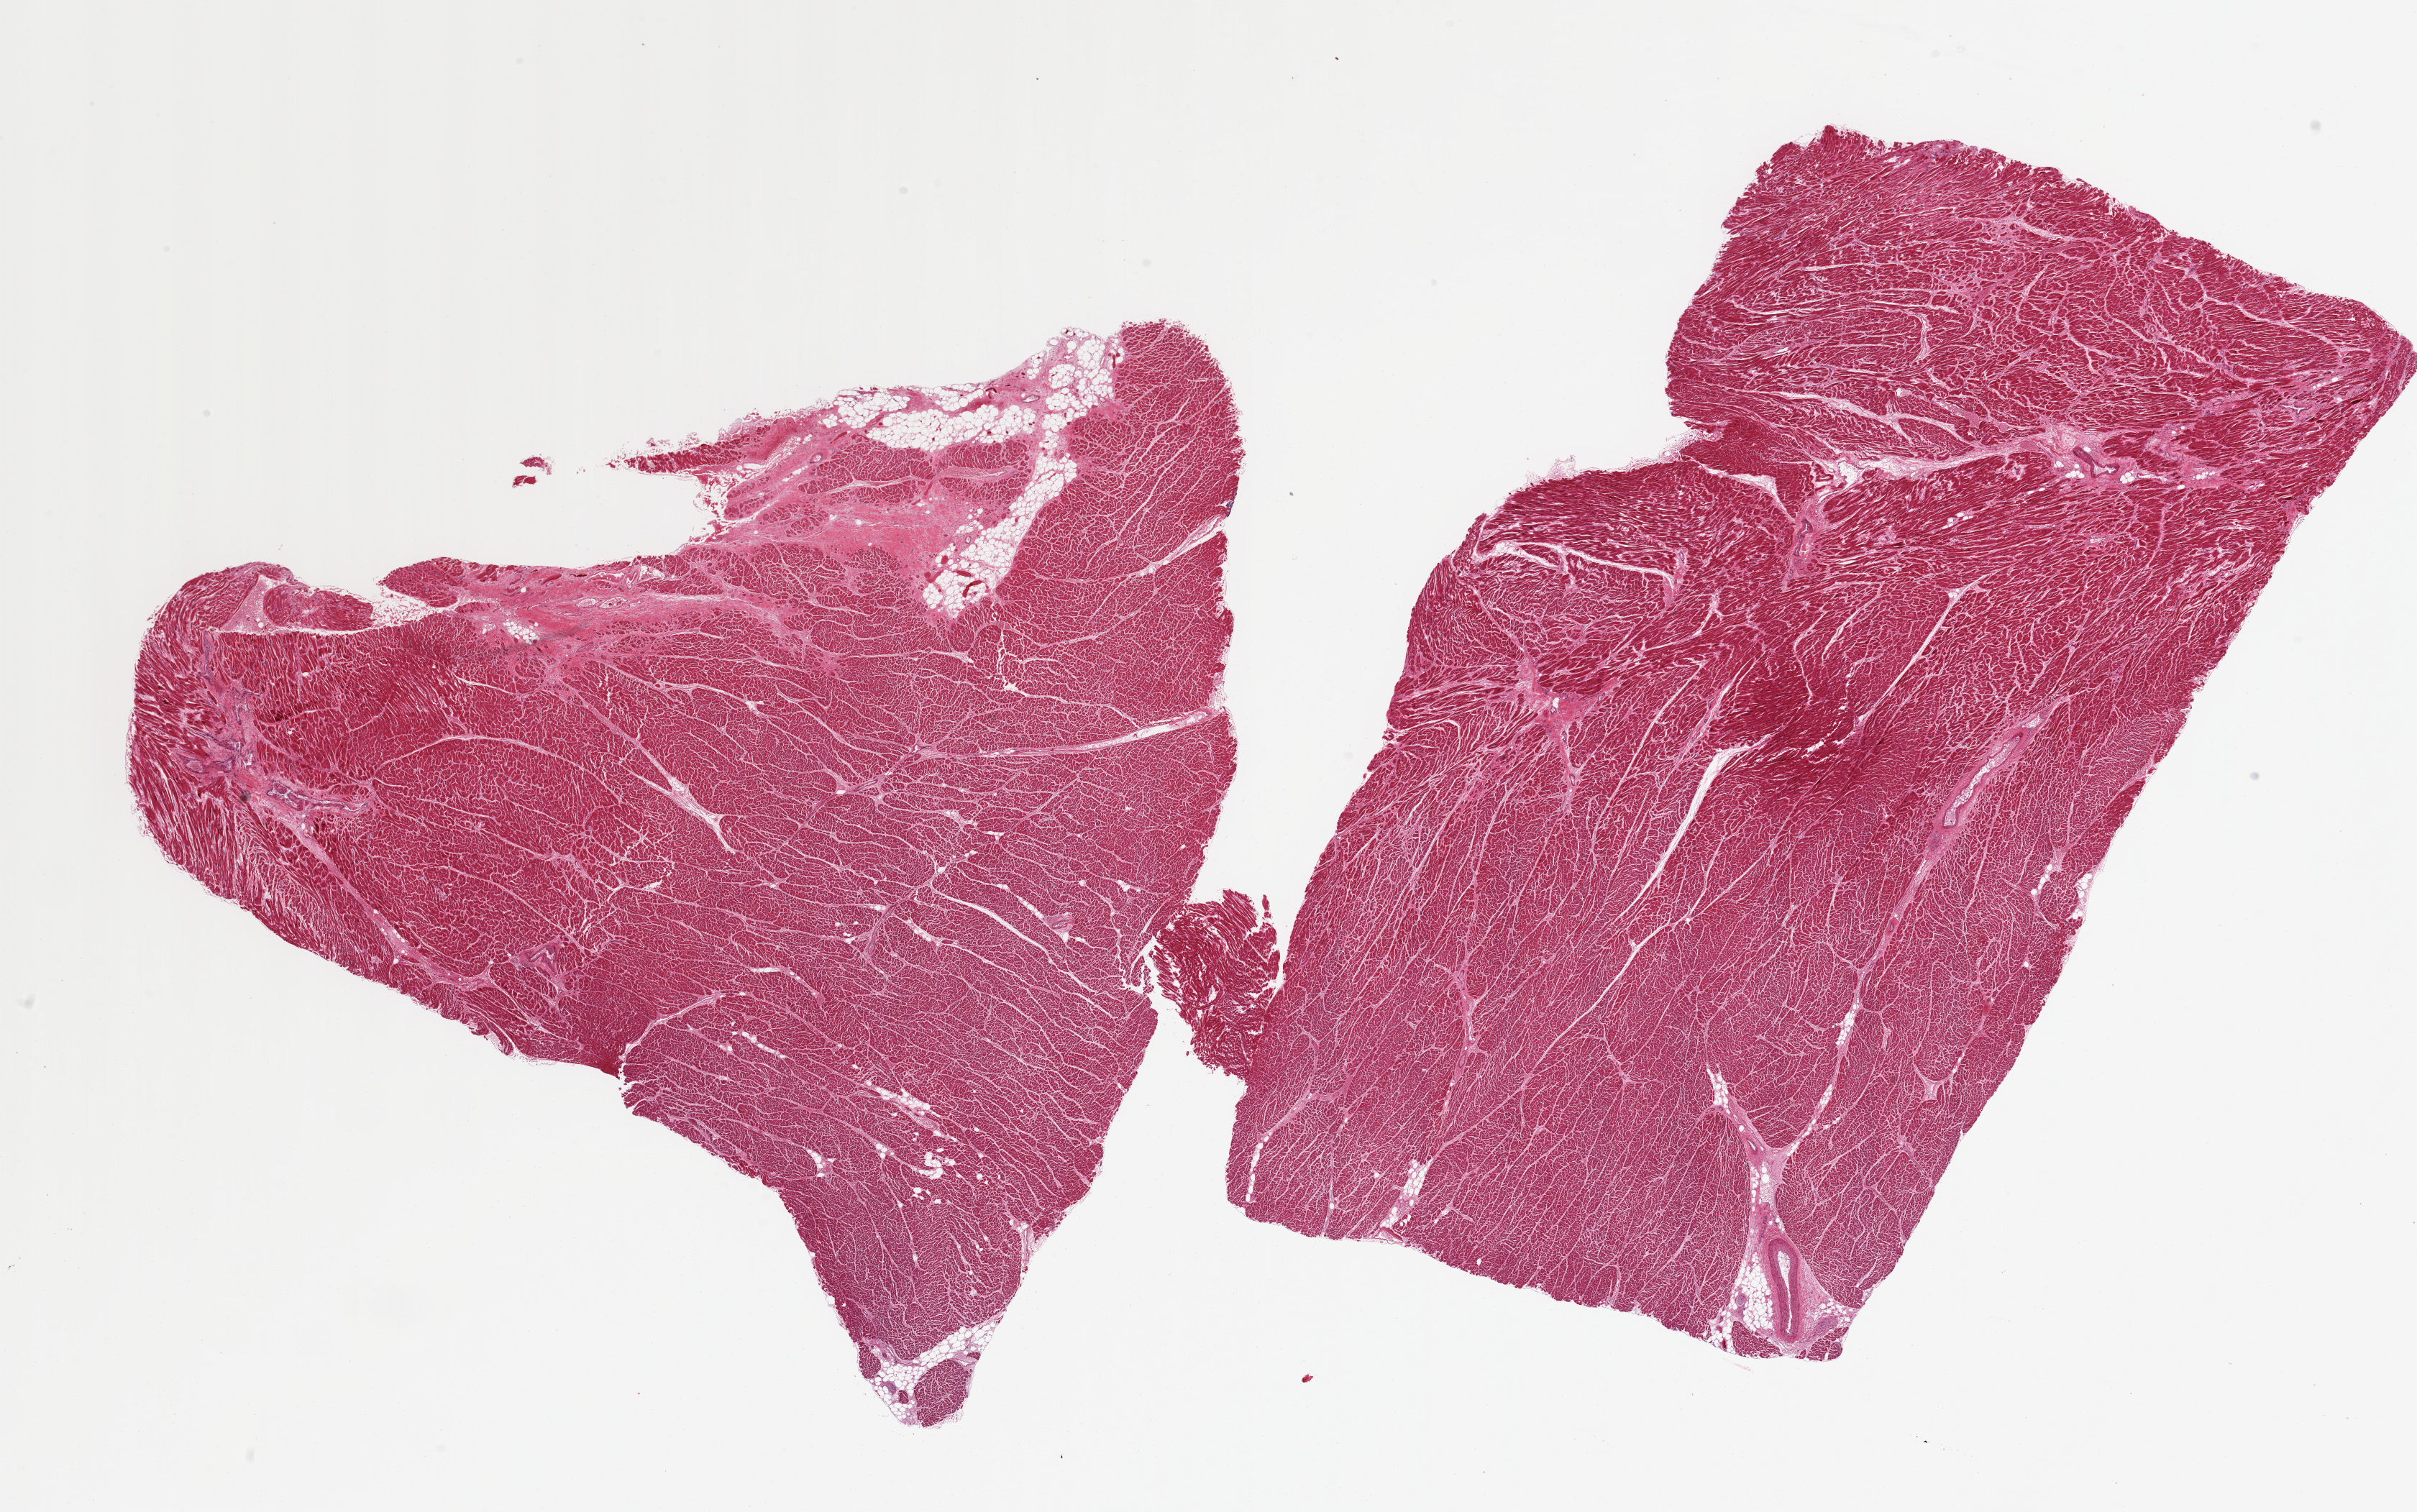
H&E whole-slide image, a low-resolution overview of the entire scanned area, about 26.6 x 16.6 mm (slide scanned at 20x). PAXgene-fixed, paraffin-embedded tissue. Sampled site (target tissue): heart. Donor tissue sample. Donor: male.
Reviewer comment on this tissue sample: 2 pieces: fat and interstitial fibrosis with scarring; multifocal fiber eosinophilia.